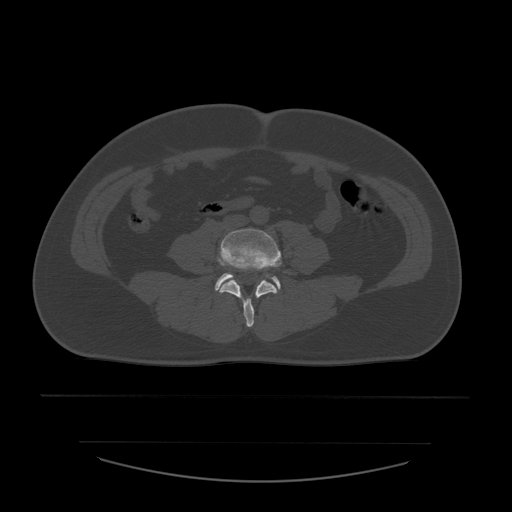
CT including the spine, one axial slice. Reconstruction kernel STANDARD. Bone window (W 1800 / L 400 HU). 512 × 512 image matrix. Patient age 44 years. Case-level facts recorded for this patient, not image findings: primary cancer: soft tissue sarcoma.
Outlined on this slice (semi-automatic segmentation, software-assisted and operator-edited):
- L4 vertebra: bounding box (x1, y1, x2, y2) in pixels: (217, 229, 282, 328)
- L5 vertebra: (215, 274, 281, 291)